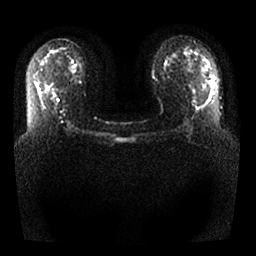
Breast MRI, one axial slice; slice 18 of 25 in the series (ordered by position); diffusion-weighted series; image 2 of 4 stored at this slice position (different b-values; order by instance number); 1.5 T; 4 mm slice thickness; 256 × 256 image matrix. Female patient.
Outlined on this slice (expert manual segmentation):
- tumour on diffusion-weighted imaging: bounding box <210,80,213,85> (left, top, right, bottom; pixels)